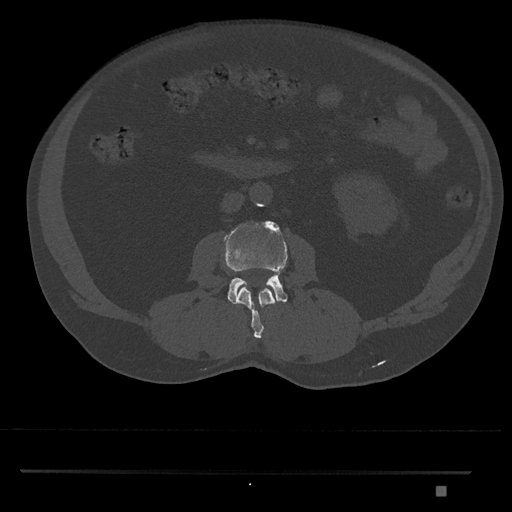
CT including the spine, one axial slice; position 713 of 1134 along the scan axis; bone window (W 1800 / L 400 HU); 512 × 512 image matrix, field of view 429 × 429 mm. Male patient, age 65 years. Case-level facts recorded for this patient, not image findings: primary cancer: prostate.
Structures marked on this image (semi-automatic segmentation, software-assisted and operator-edited):
- L2 vertebra: bounding box (x1, y1, x2, y2) in pixels: (237, 286, 276, 339)
- L3 vertebra: (223, 221, 288, 306)